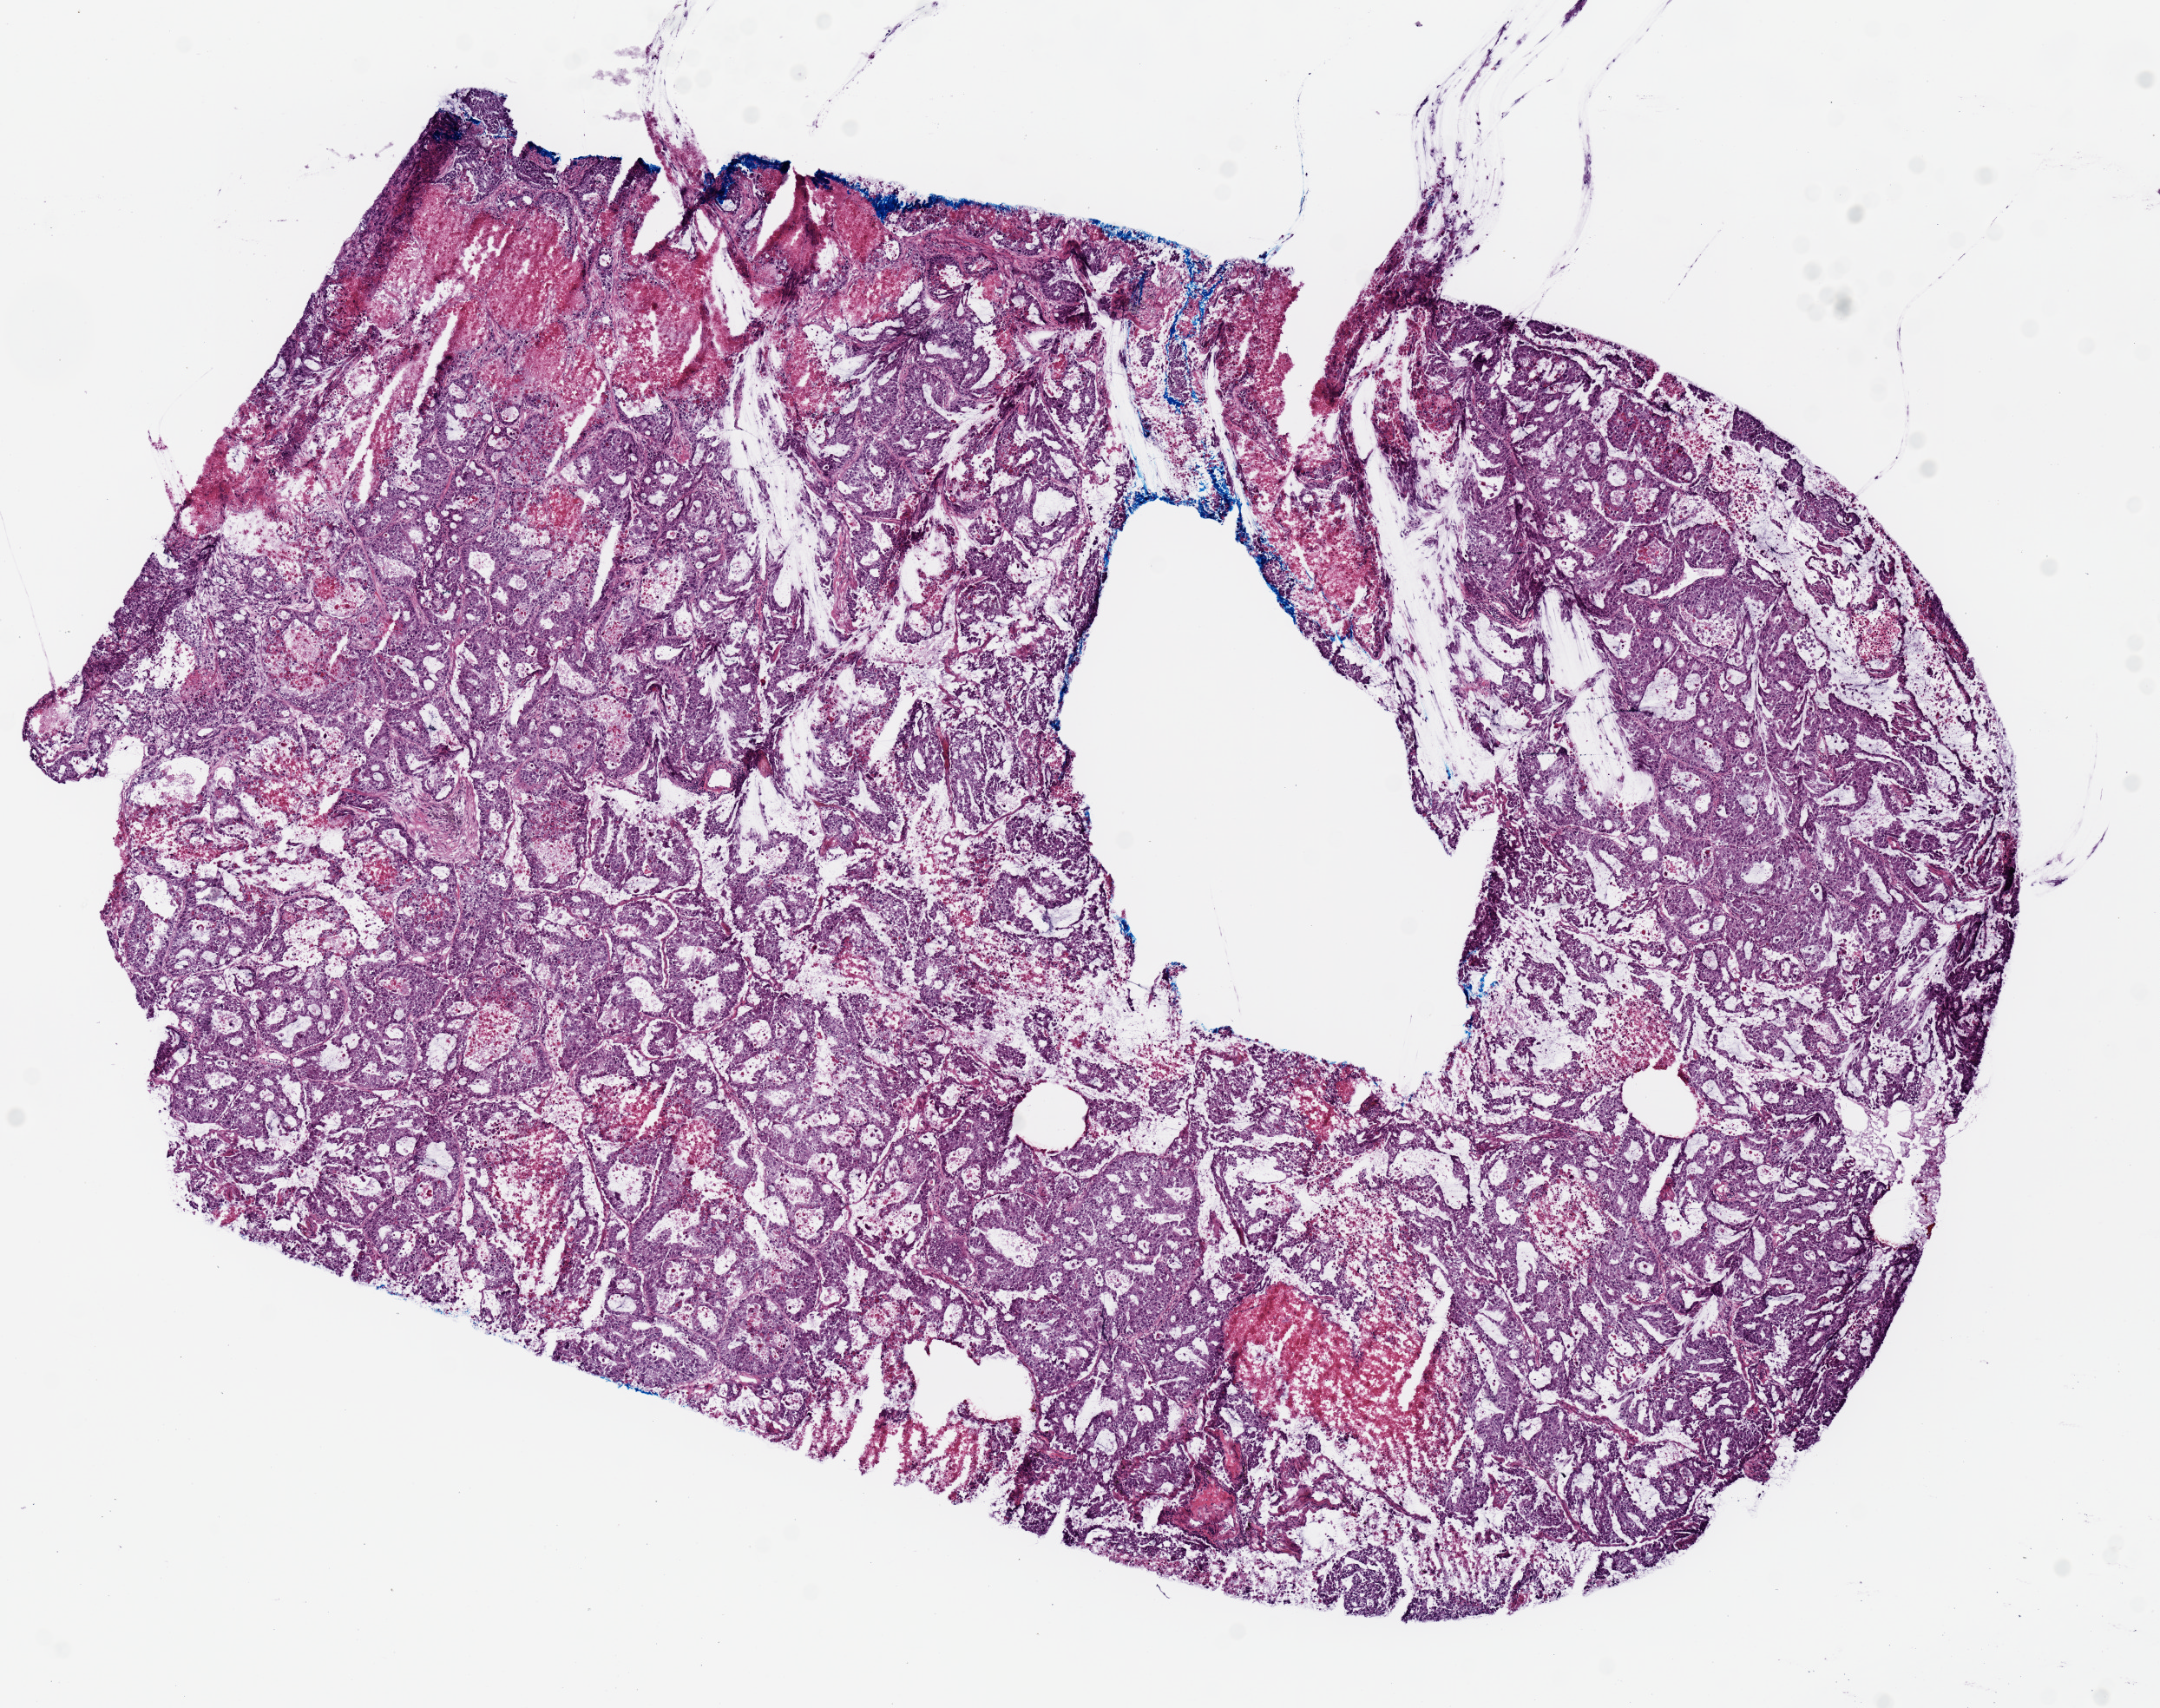
H&E whole-slide image, shown as a low-resolution overview of the whole scanned area (about 9.8 x 7.8 mm, slide scanned at 20x). Frozen section from the top of the tissue portion. Sample: primary tumour, lung. Male patient; age at initial diagnosis 51 years. Pathologist review of this section (percent, as recorded): tumour cells 70%, tumour nuclei 85%.
Pathologic diagnosis: Adenocarcinoma, NOS (upper lobe, lung).